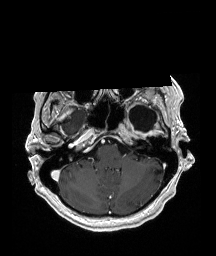
Brain MRI from a brain-tumour surgery series, one axial slice; position 147 of 192 along the scan axis; T1-weighted post-contrast; 1 mm slice thickness; 216 × 256 image matrix, field of view 211 × 250 mm. Case-level facts recorded for this patient, not image findings: histopathology: Glioblastoma; WHO grade: 4; IDH mutation: no; tumour location: Left Temporal.
Annotated regions visible in this slice (expert manual segmentation):
- previous resection cavity: bounding box [x1, y1, x2, y2] px = [128, 106, 157, 132]